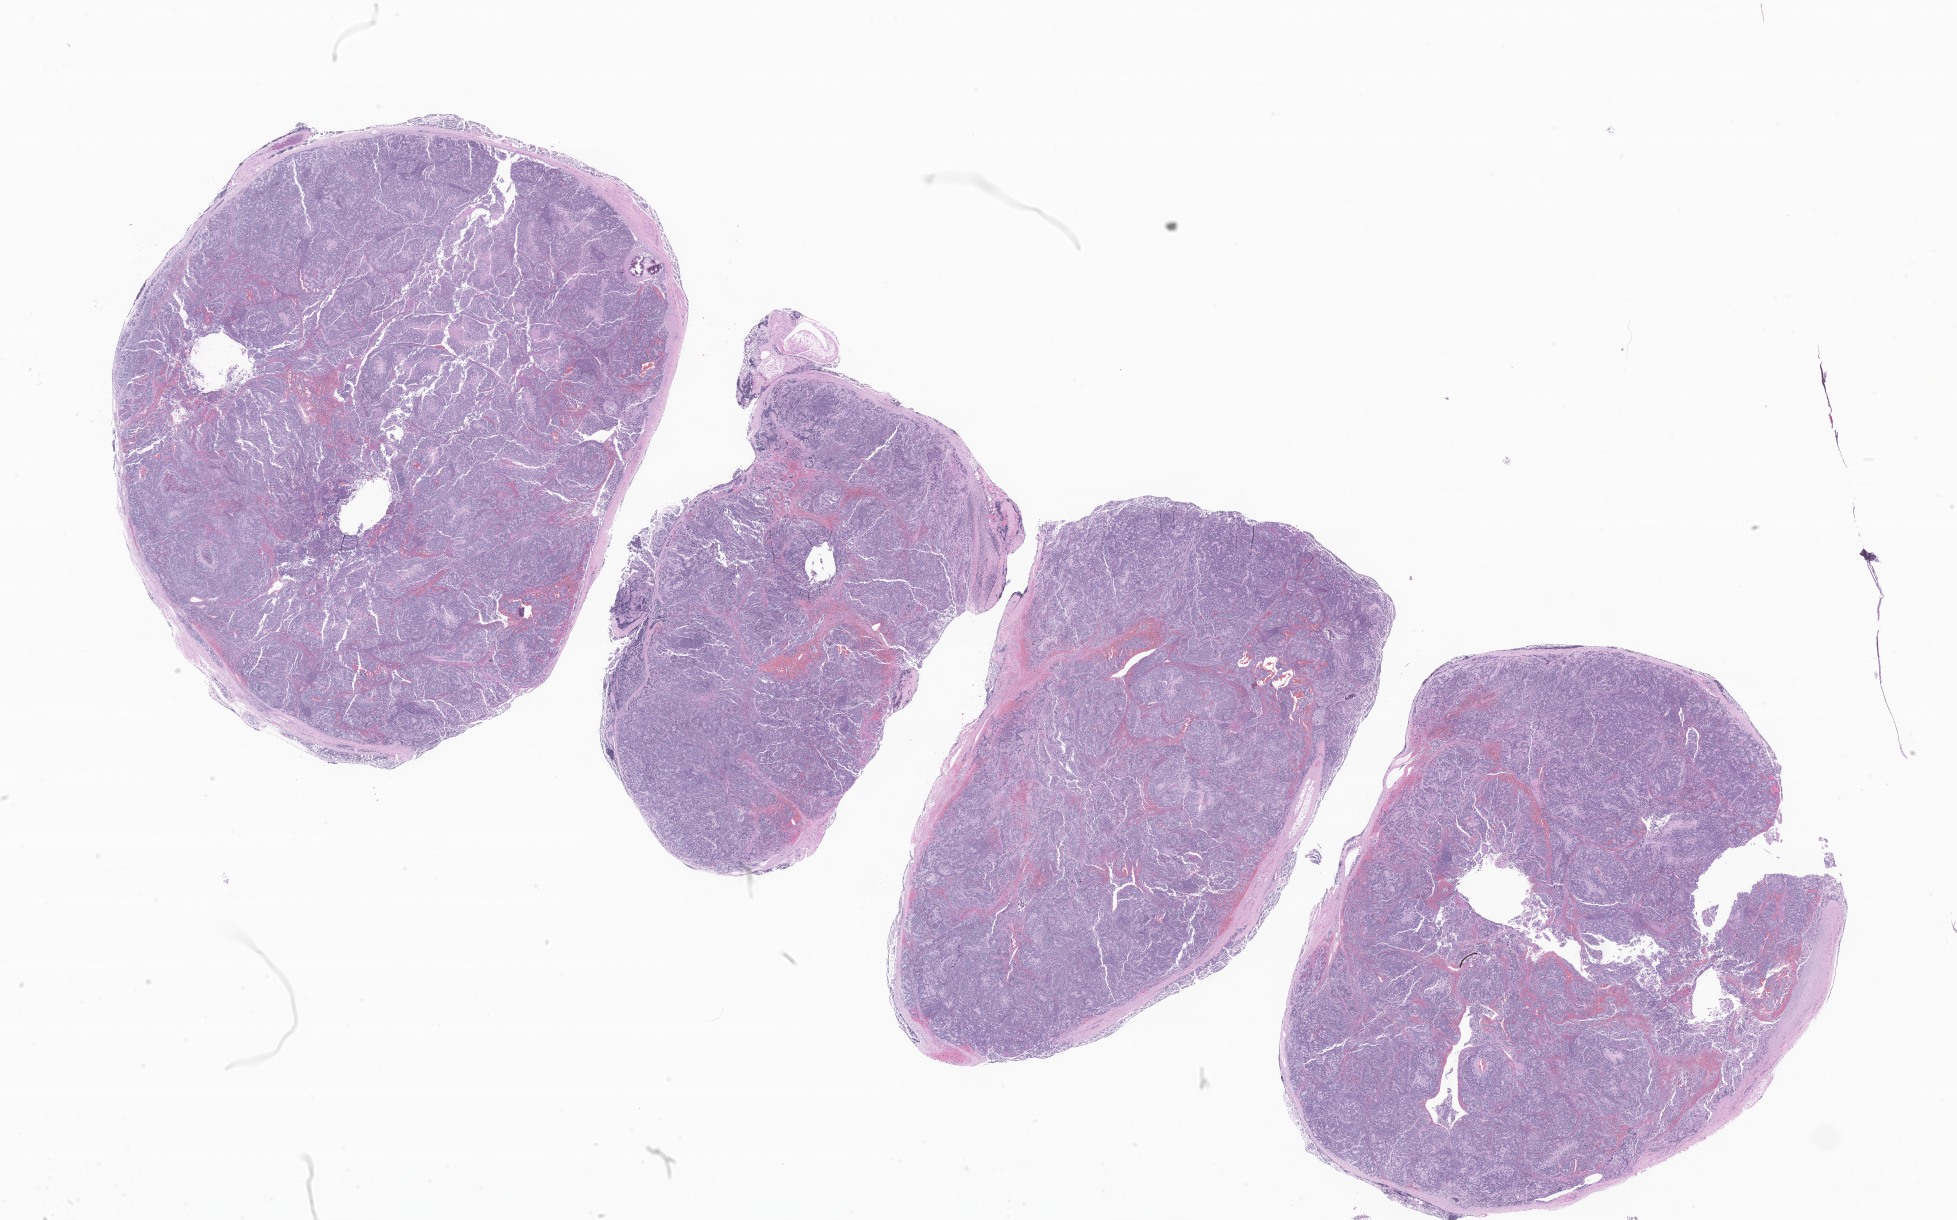
H&E whole-slide image of tumor tissue from the mediastinum, a low-resolution overview of the entire scanned area, about 33.0 x 20.6 mm; formalin-fixed, paraffin-embedded (FFPE) tissue. Patient female; age 266 days.
* recorded diagnosis: Neoplasm, uncertain whether benign or malignant